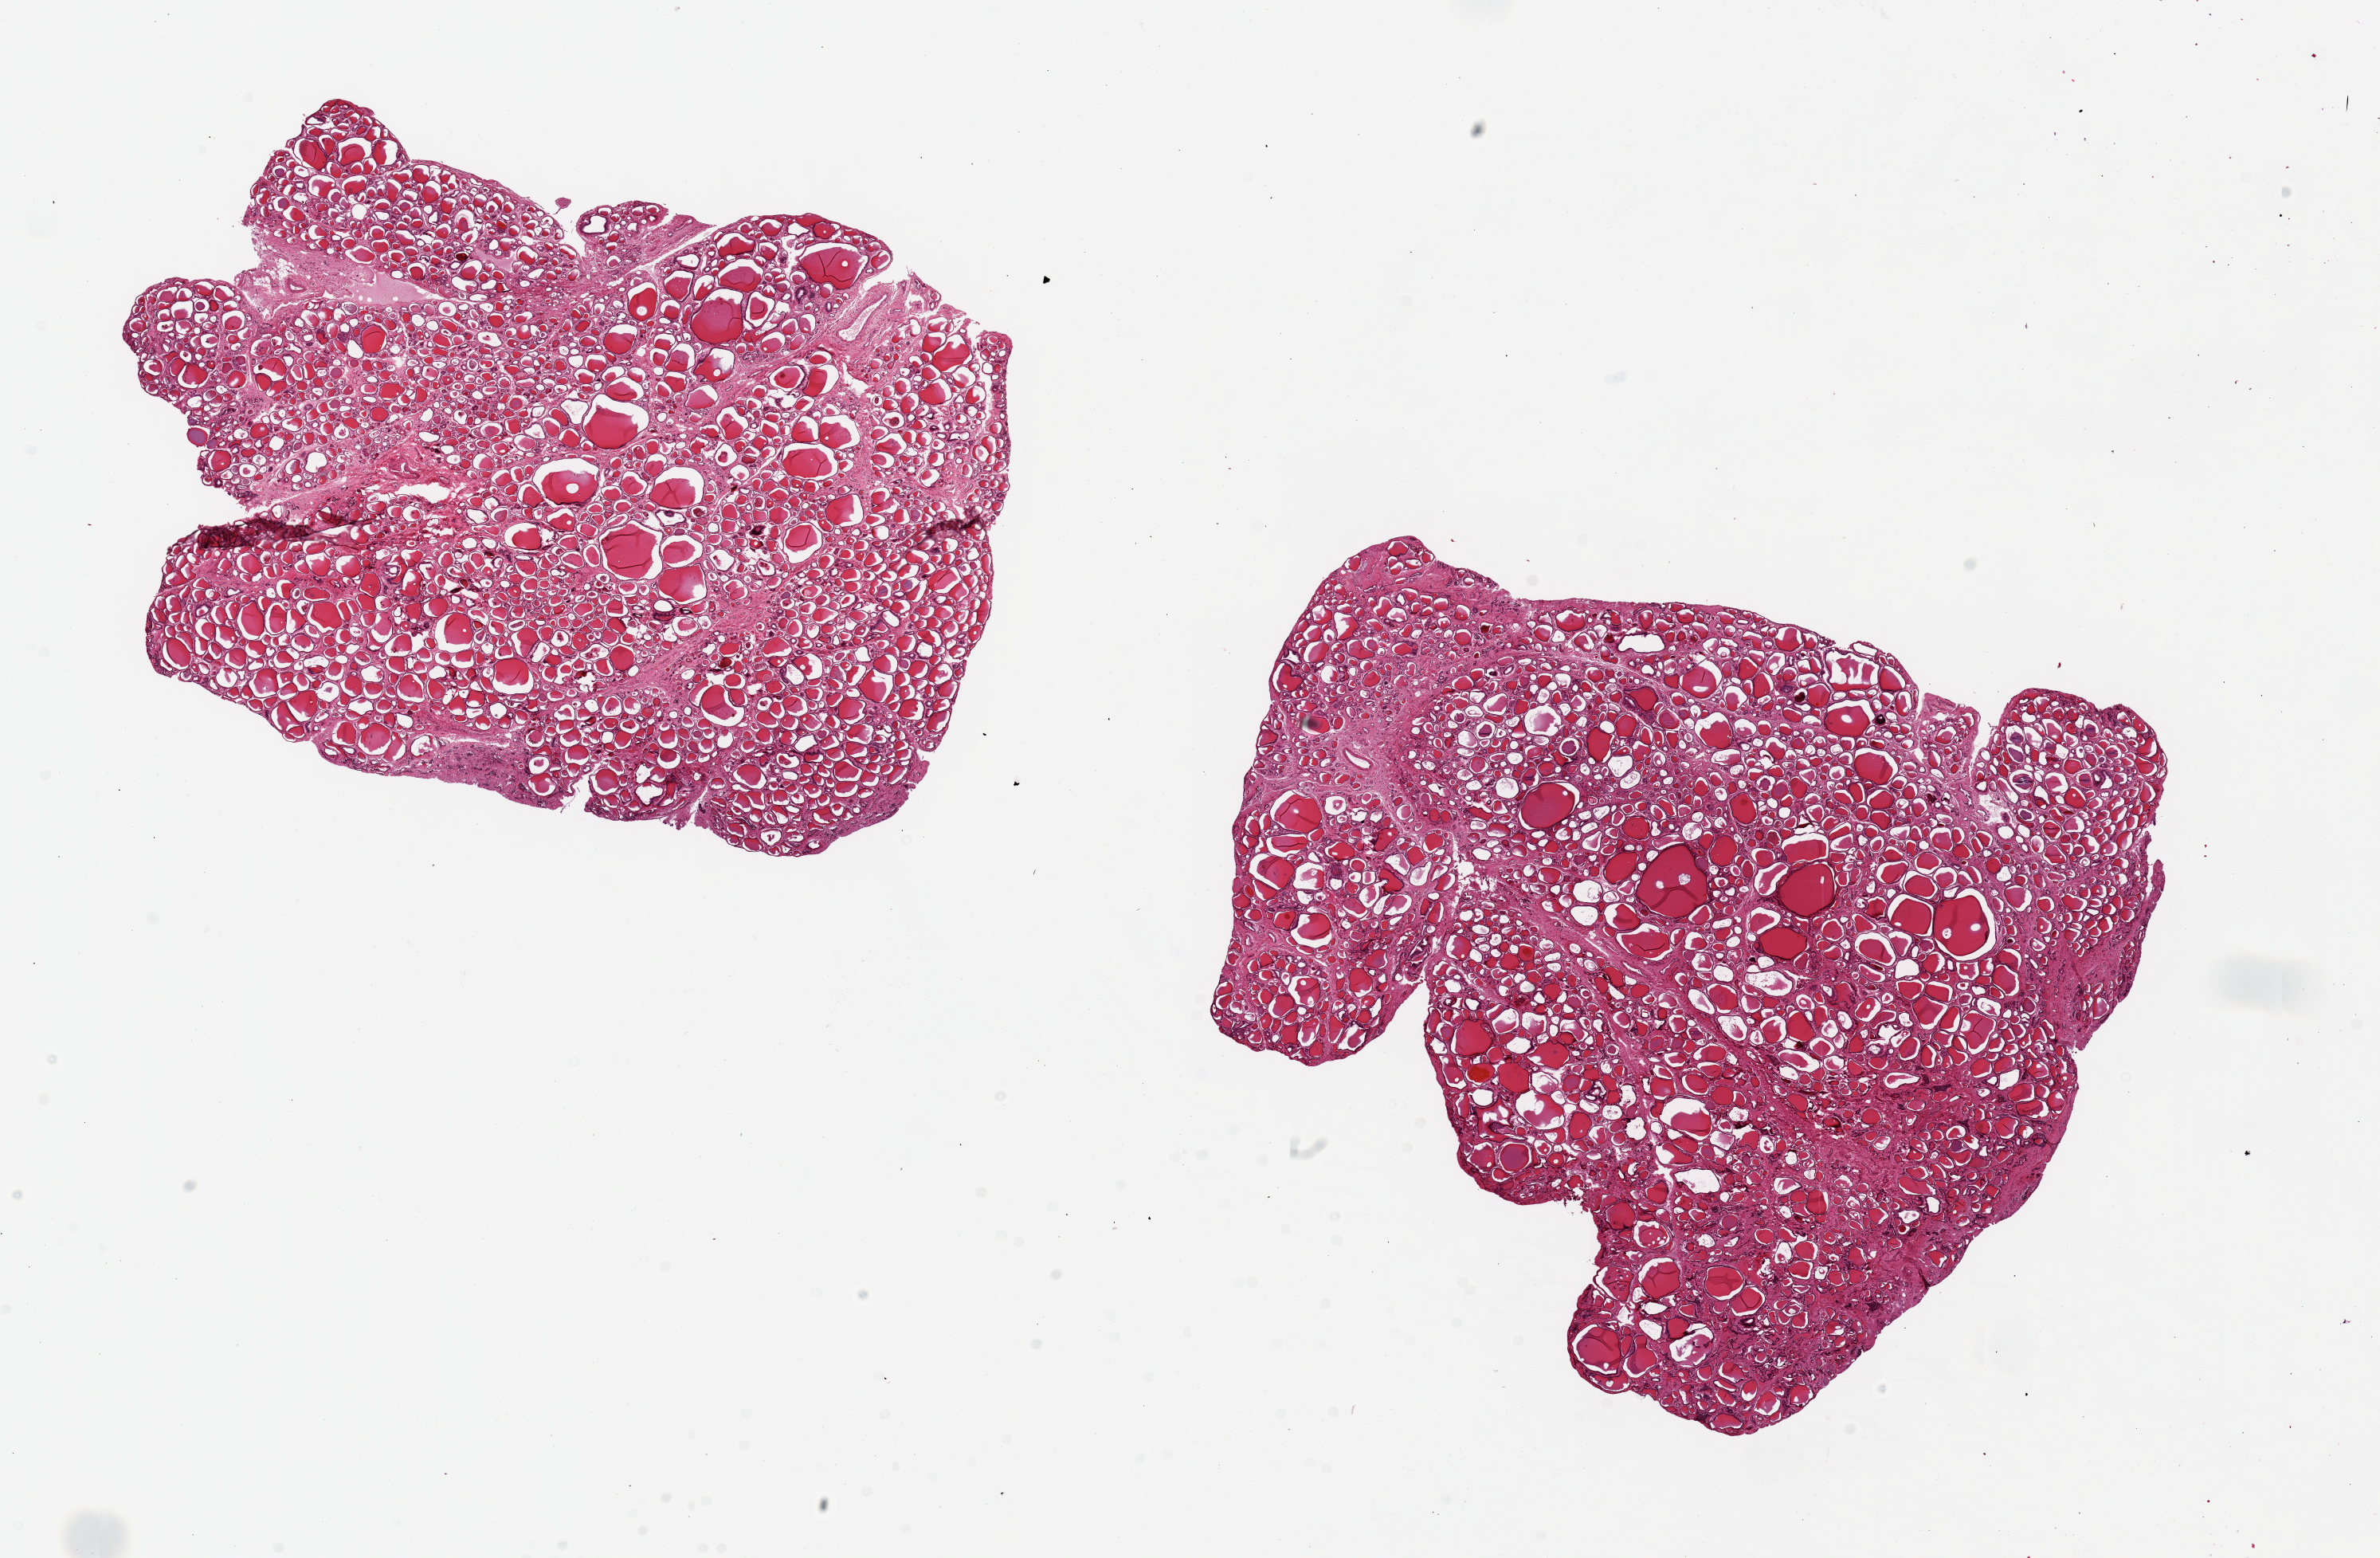
Whole-slide image, hematoxylin and eosin (H&E) stain, shown as a low-resolution overview of the whole scanned area (about 23.6 x 15.5 mm, acquisition: 20x scan), PAXgene-fixed paraffin-embedded (PFPE) section, target tissue: thyroid, tissue donor sample. Donor sex: male.
Reviewer comment on this tissue sample: 2 pieces, 9x6.5 & 9x8mm; interstitial fibrosis.